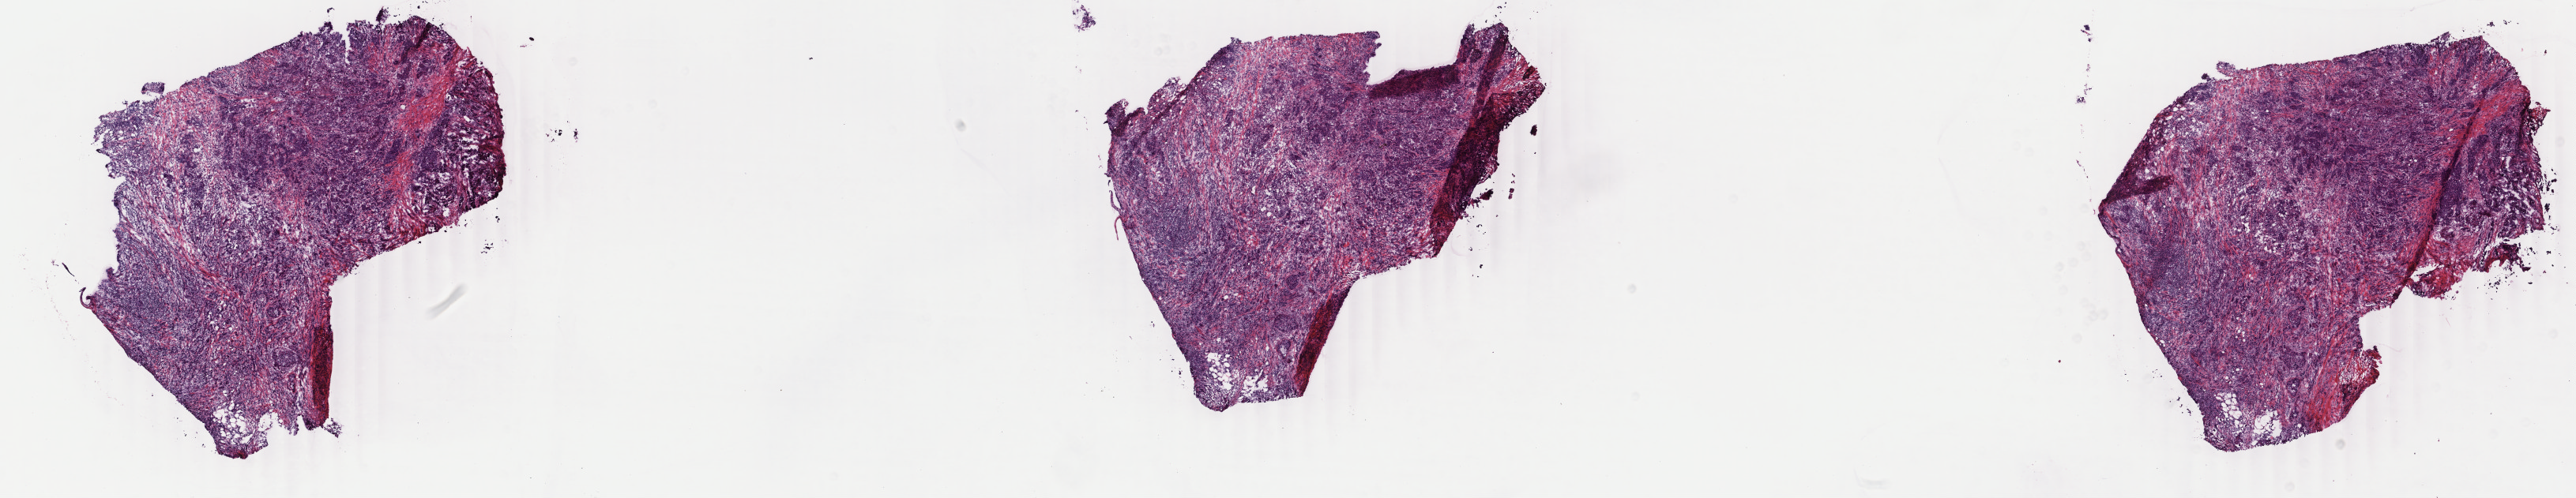
H&E-stained whole-slide image — whole scanned area (about 25.9 x 5.0 mm, acquisition: 40x scan) shown as a low-resolution overview. Frozen section from the bottom of the tissue portion. Sample: primary tumour, breast. Female patient; age at initial diagnosis 40 years. Pathologist review of this section (percent, as recorded): tumour cells 80%, tumour nuclei 80%, normal cells 0%, stromal cells 15%, necrosis 5%. Infiltration values recorded for this section: lymphocyte infiltration 20%, monocyte infiltration 10%, neutrophil infiltration 10%.
AJCC pathologic stage: IIA (6th edition). Pathologic diagnosis: Infiltrating duct carcinoma, NOS. Laterality: left. Lymph nodes positive (case pathology): 0 of 1 examined.